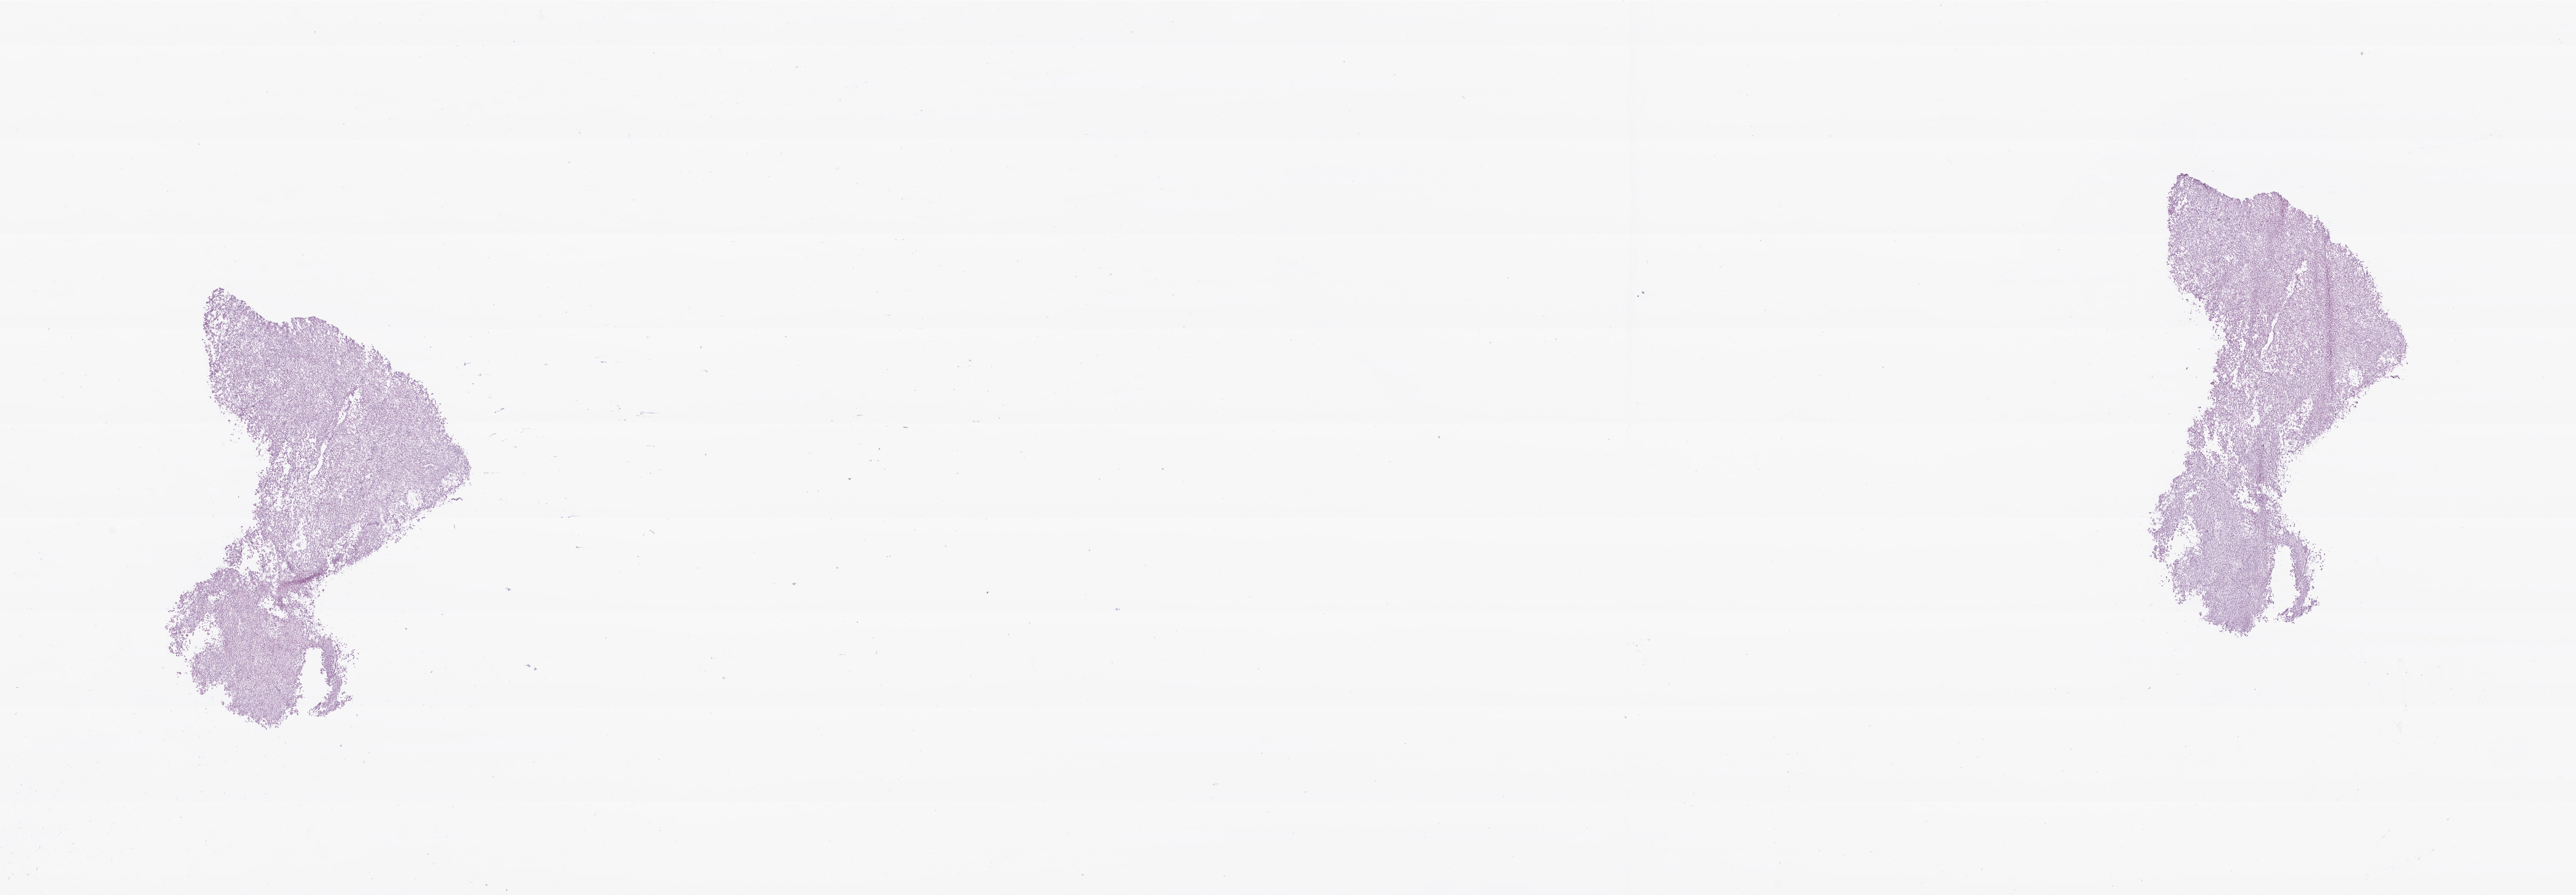
Hematoxylin and eosin (H&E) whole-slide image of tumor tissue from the adrenal gland — whole scanned area (about 29.0 x 10.1 mm) shown as a low-resolution overview; frozen section. Patient: female, age 178 months (14 years 10 months).
• diagnosis: Carcinoma, NOS